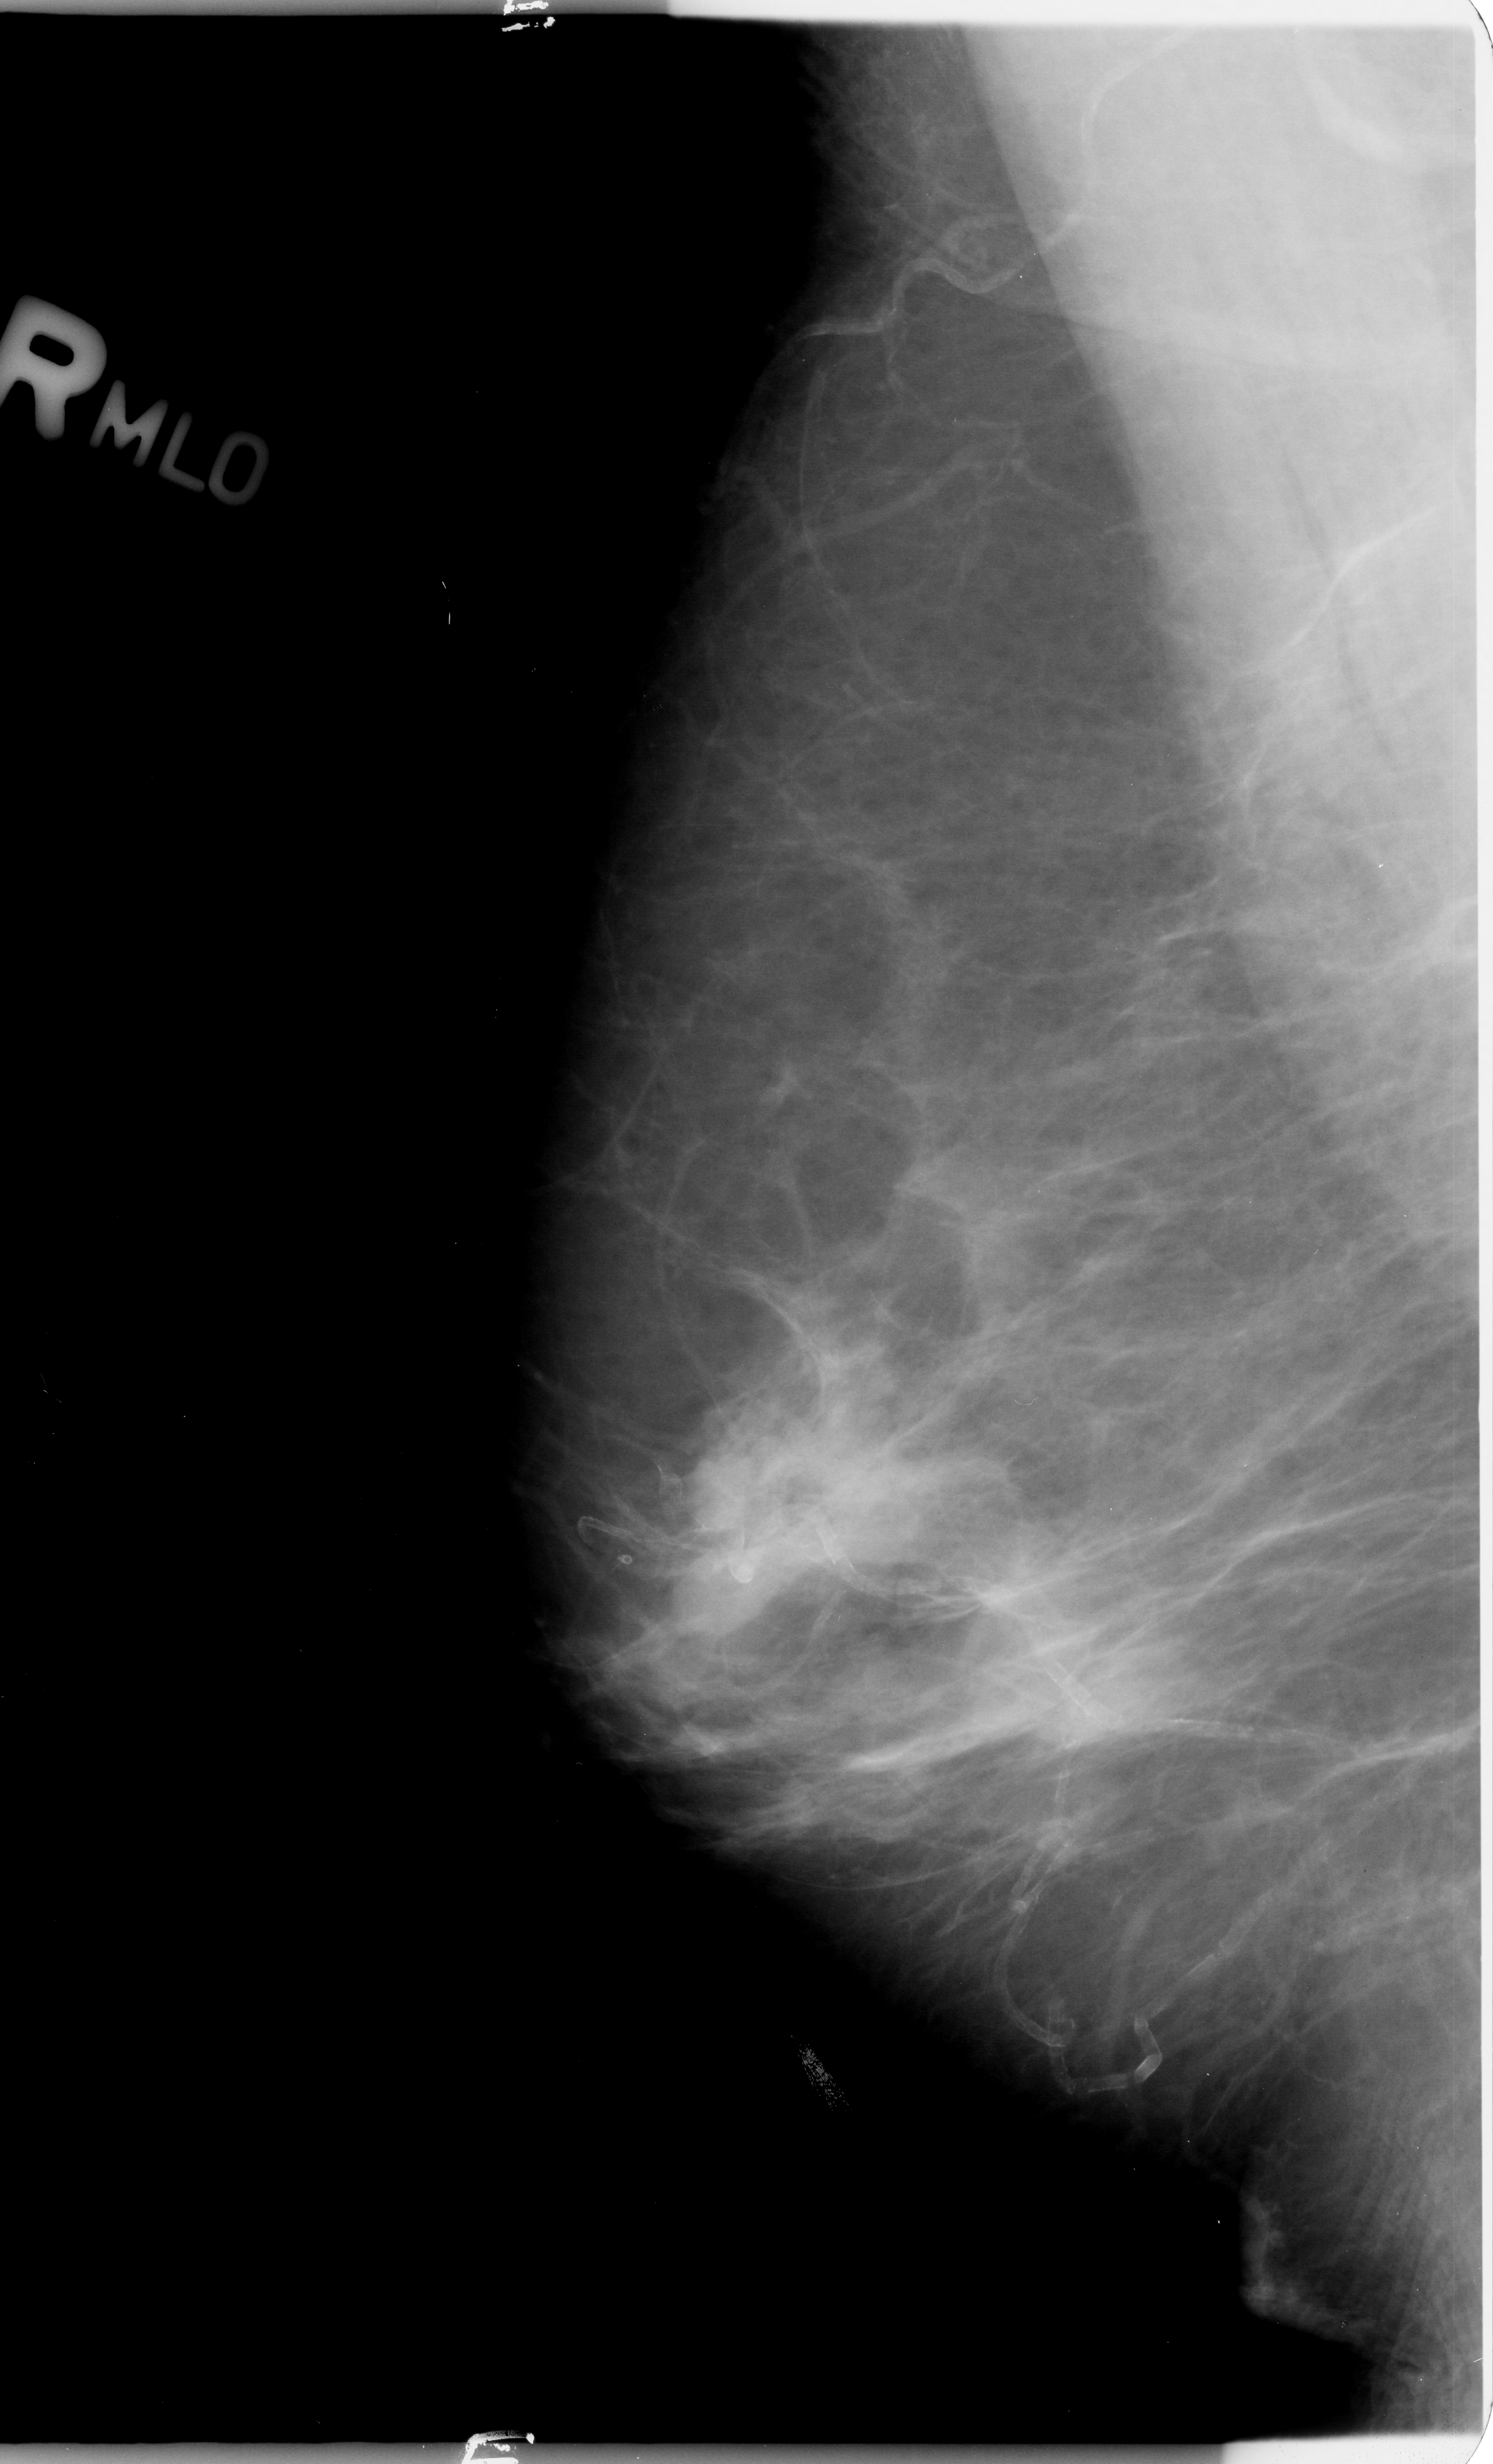
Digitized screen-film mammogram. Right breast. MLO view. Breast composition: heterogeneously dense (BI-RADS density category 3 of 4). 1493 × 2464 image matrix.
Marked abnormalities (boxes around the expert regions of interest):
- mass, shape irregular, margins obscured / ill defined; BI-RADS assessment category 3; subtlety rating 2 on a 1 (subtle) to 5 (obvious) scale; pathology result (as recorded, not read from the image): malignant: box from (x=671, y=1438) to (x=781, y=1553) px